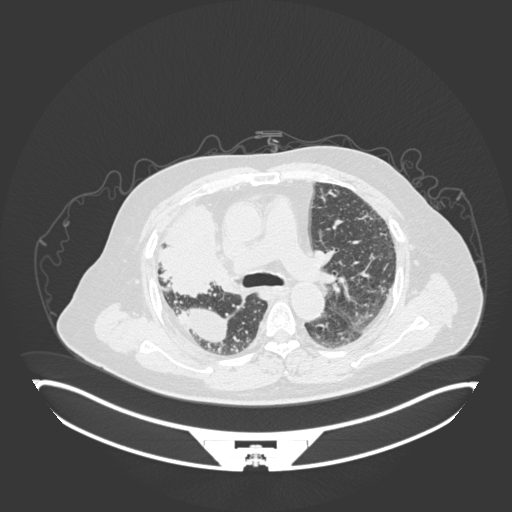
Chest CT, one axial slice. Reconstruction kernel B30f. 120 kVp. Lung window (W 1500 / L -600 HU). 512 × 512 image matrix, field of view 500 × 500 mm. Male patient, age 69 years. Case-level facts recorded for this patient, not image findings: clinical TNM (as recorded): T4 N3 M1.
Annotated regions visible in this slice (bounding box drawn by a radiologist):
- lung tumour (recorded histology: adenocarcinoma): bounding box (x1, y1, x2, y2) in pixels: (157, 199, 226, 297)